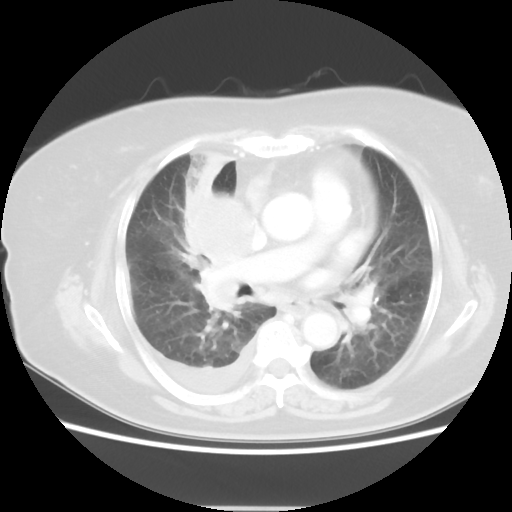
Chest CT, one axial slice; position 27 of 48 along the scan axis; reconstruction kernel STANDARD; lung window (W 1500 / L -600 HU); 512 × 512 image matrix, field of view 360 × 360 mm. Patient: female, 73 years. Case-level facts recorded for this patient, not image findings: clinical TNM (as recorded): T3 N3 M1b.
Annotated regions visible in this slice (rectangle marked by the reading radiologist):
- lung tumour (recorded histology: small cell carcinoma): bounding box (x1, y1, x2, y2) in pixels: (184, 142, 257, 324)